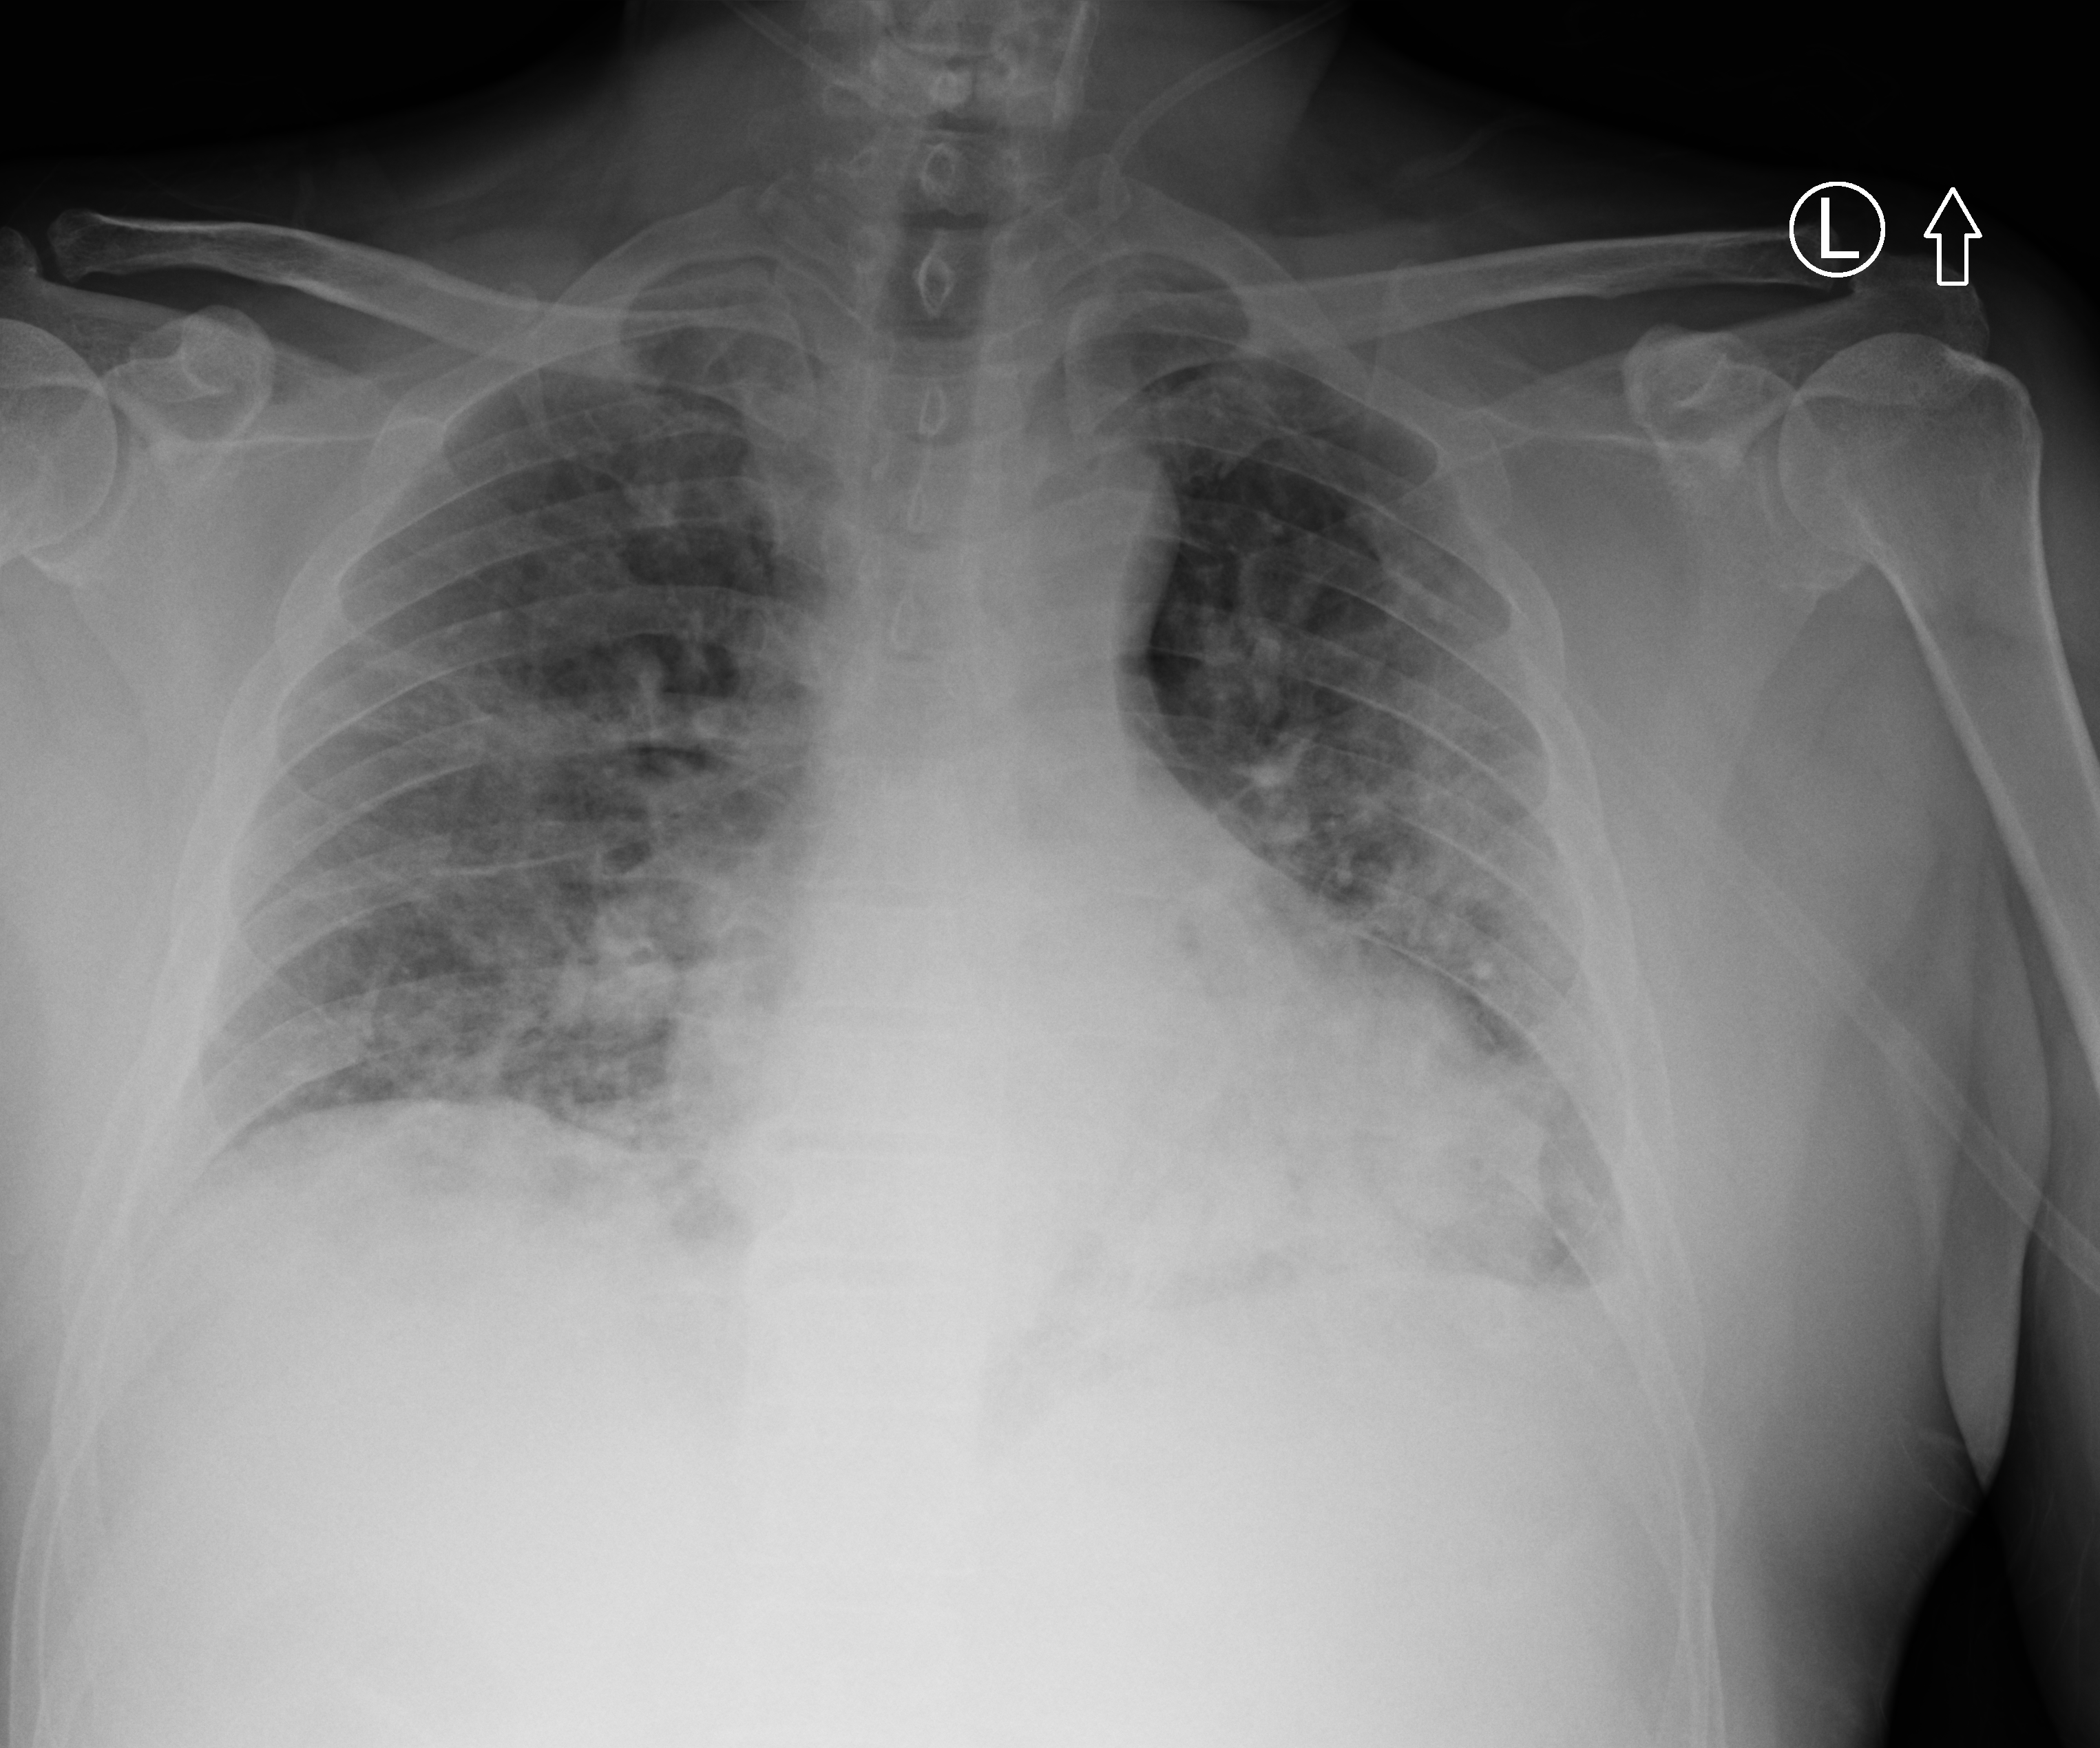
Chest X-ray (portable). Patient hospitalised with COVID-19; male, aged 60–74 years.
Admission-level facts for this patient (not findings on this image; timing relative to this image not recorded):
- admitted to intensive care during this hospital stay: no
- mechanically ventilated during this hospital stay: no
- length of hospital stay: 11 days